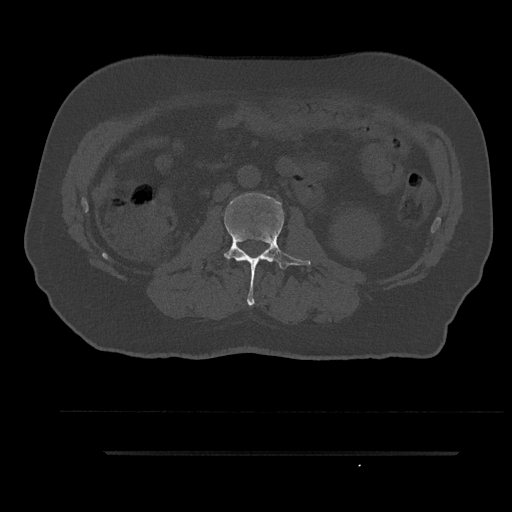
CT including the spine, one axial slice. Position 105 of 797 along the scan axis. Reconstruction kernel Br40s/3. 120 kVp. Bone window (W 1800 / L 400 HU). 0.5 mm slice thickness. 512 × 512 image matrix, field of view 432 × 432 mm. Patient: male, 63 years. Case-level facts recorded for this patient, not image findings: primary cancer: renal; vertebrae with lytic lesions (as recorded): T8.
Outlined on this slice (semi-automatic segmentation, software-assisted and operator-edited):
- L2 vertebra: bounding box <224,193,311,306> (left, top, right, bottom; pixels)